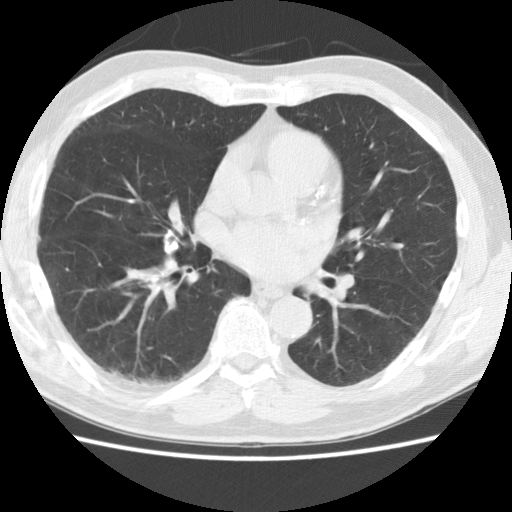
Low-dose screening chest CT, axial slice. Baseline annual screen. Lung window (W 1500 / L -600 HU). 512 × 512 image matrix. Male participant, aged 66 years at enrolment.
Lesion marked by an expert reader, bounding box [x1, y1, x2, y2] px = [132, 207, 191, 268]. Screening reader's record for this exam: no non-calcified nodule ≥4 mm recorded. Official screen result: negative screen, no significant abnormalities. Later outcome: lung cancer diagnosed 314 days after this screen — large cell neuroendocrine carcinoma, right middle lobe, poorly differentiated (G3), stage IIIA (AJCC 6th edition), 15 mm at pathology.